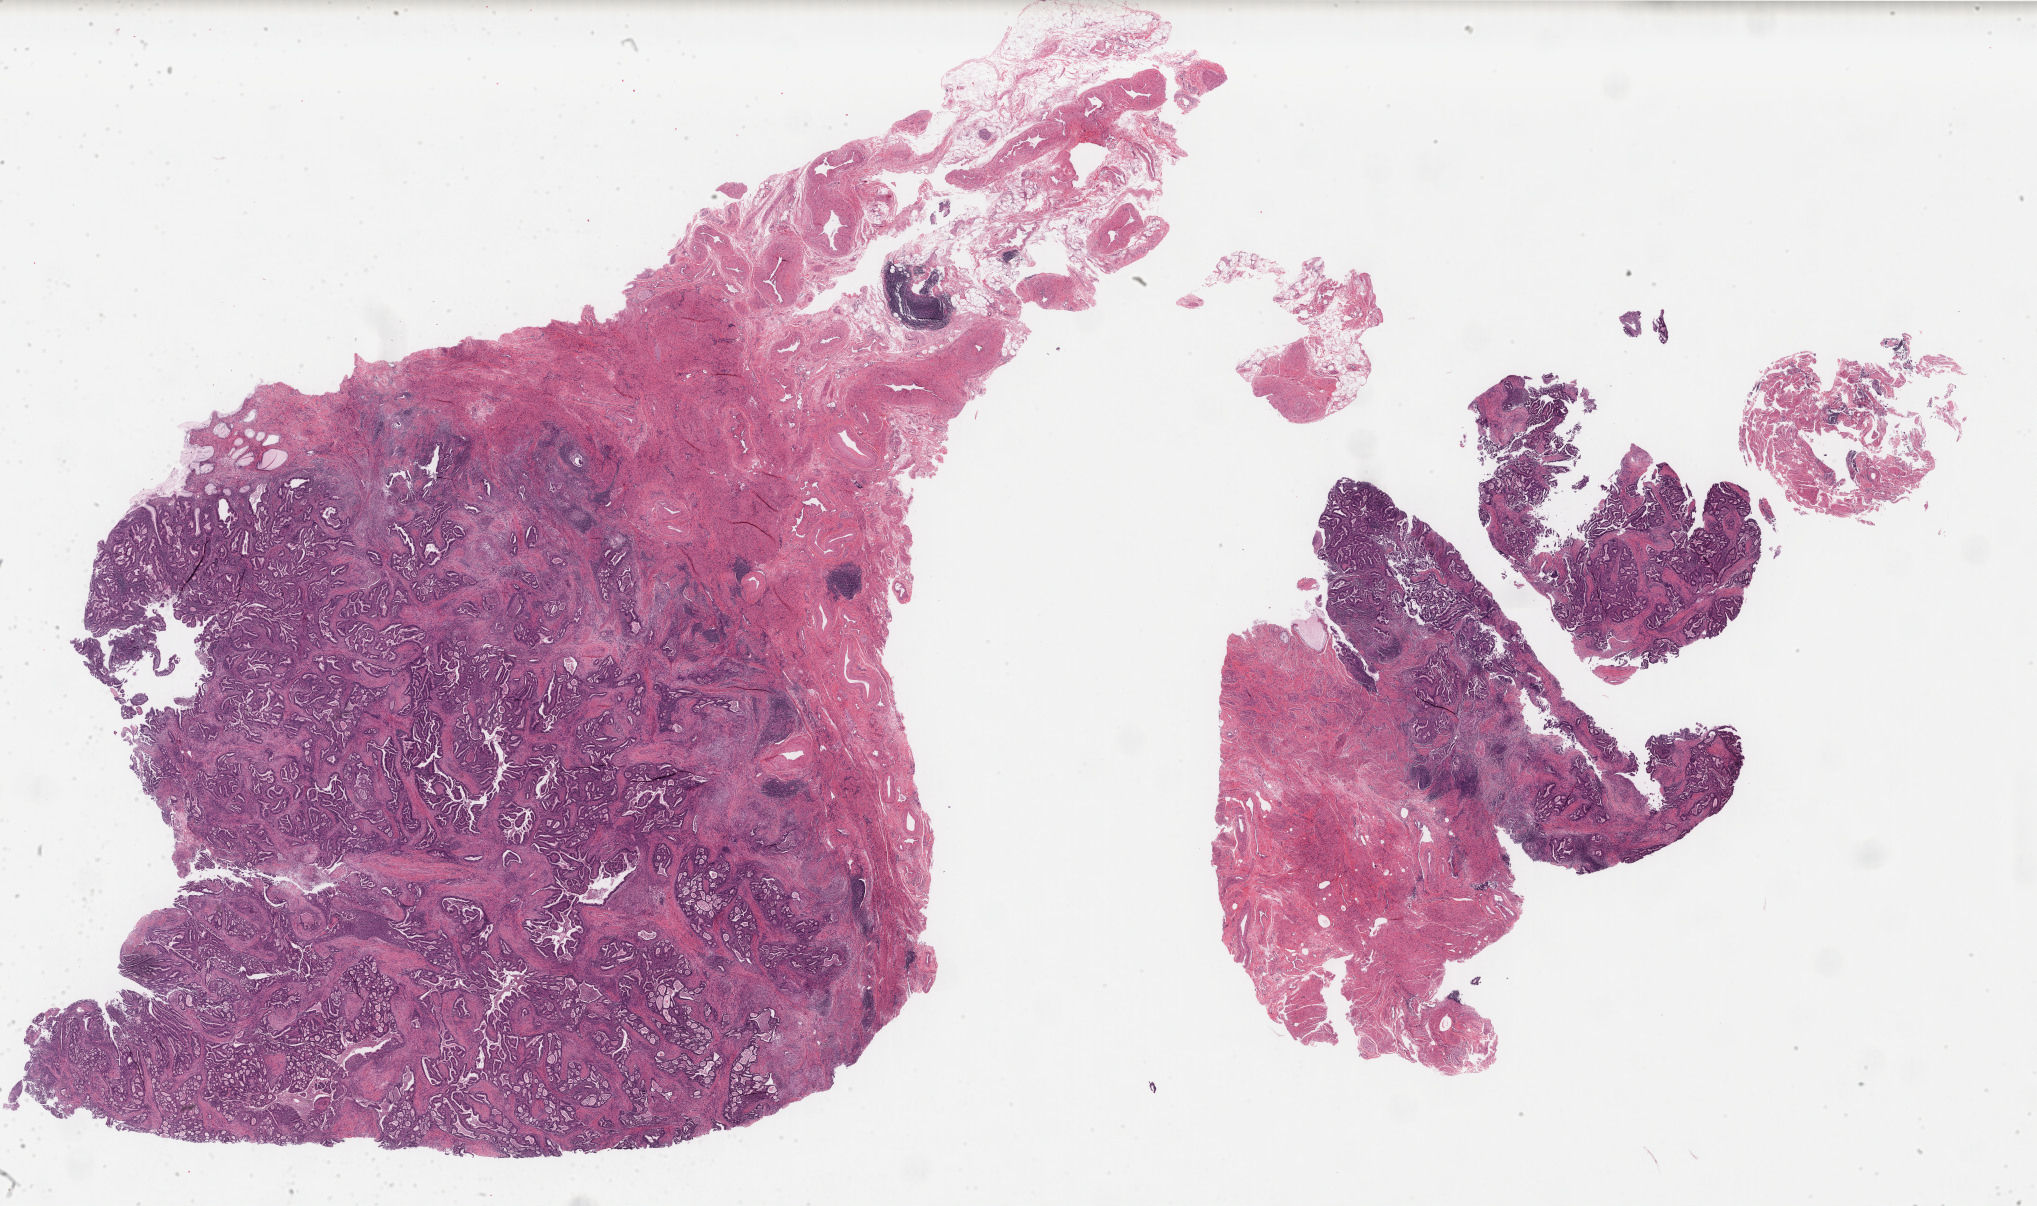
Whole-slide histology image, Hematoxylin and eosin (H&E) stained — shown as a low-resolution overview of the whole scanned area (about 32.3 x 19.1 mm, from a 40x scan), formalin-fixed paraffin-embedded (FFPE) diagnostic section, primary tumour sample from the uterus. Patient: female, age at initial diagnosis 61 years. Histologic grade: G2 (moderately differentiated).
- histologic diagnosis: Endometrioid adenocarcinoma, NOS (endometrium)
- FIGO stage: IIB